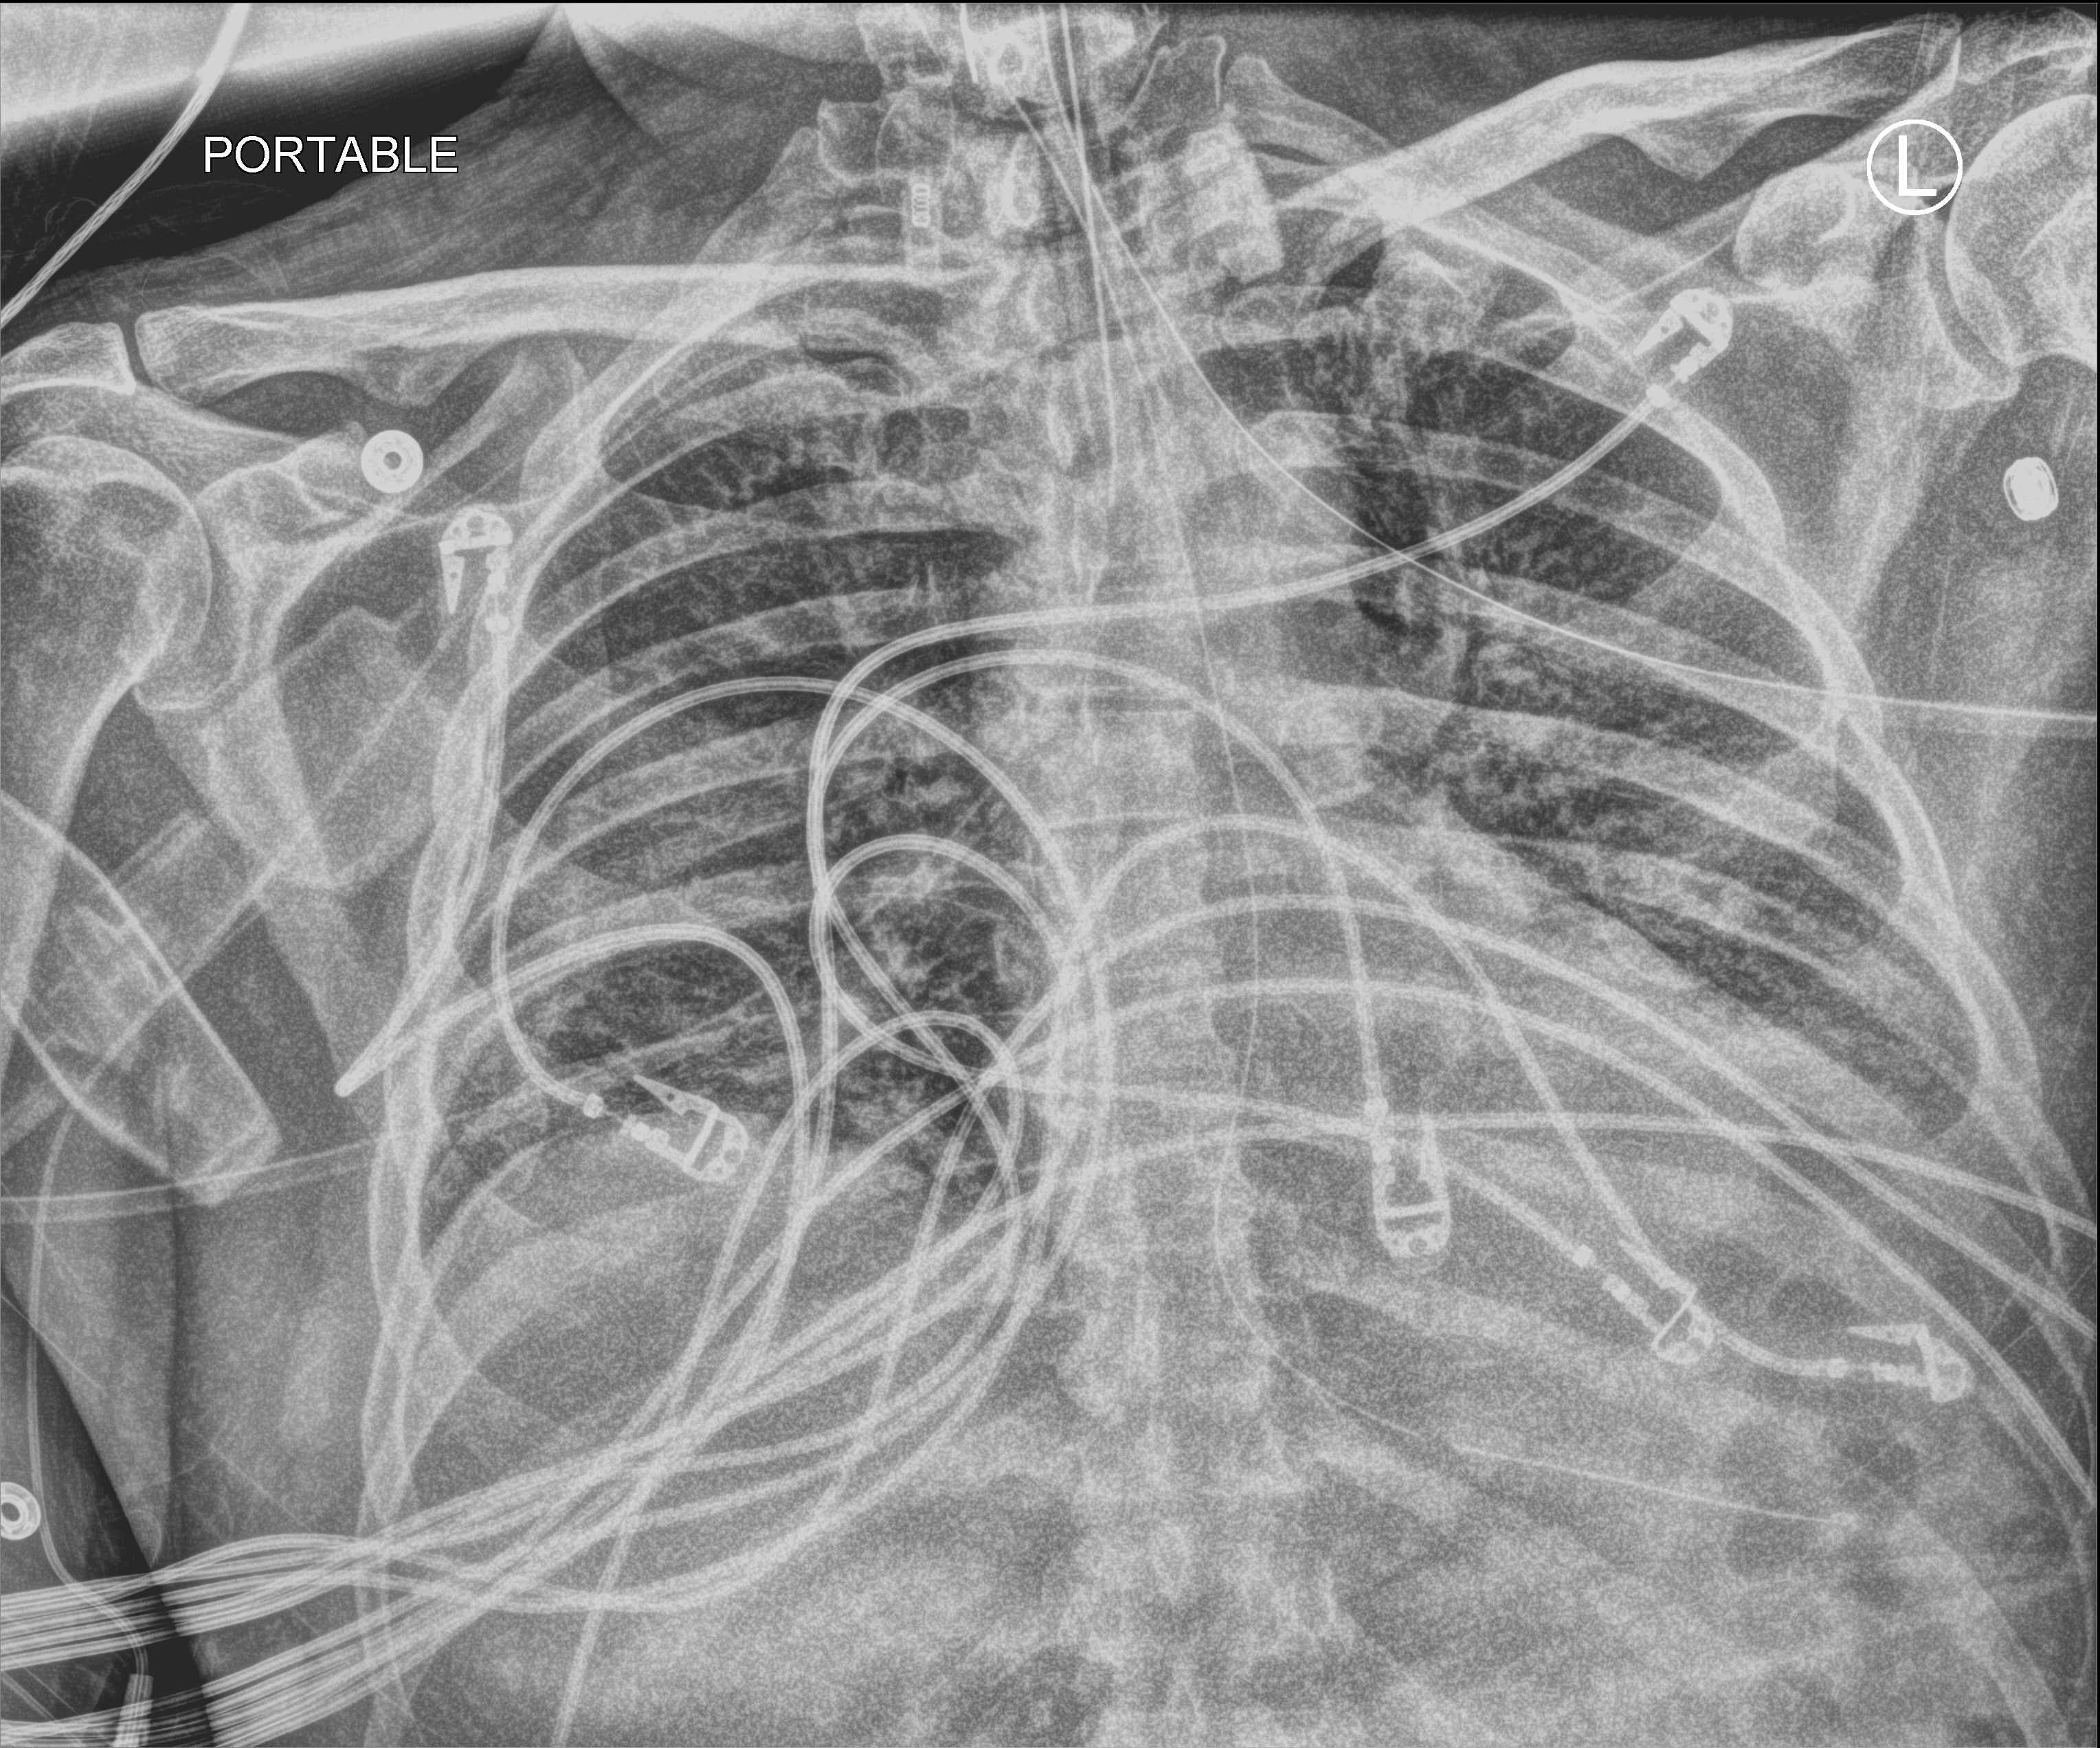
Portable chest radiograph; anteroposterior (AP) projection. Patient hospitalised with COVID-19; male, aged 60–74 years.
From the hospital-stay record, not from the radiograph (when in the stay this image was taken is not recorded): mechanically ventilated during this hospital stay: yes; COPD (admission record): no; admitted to intensive care during this hospital stay: yes.